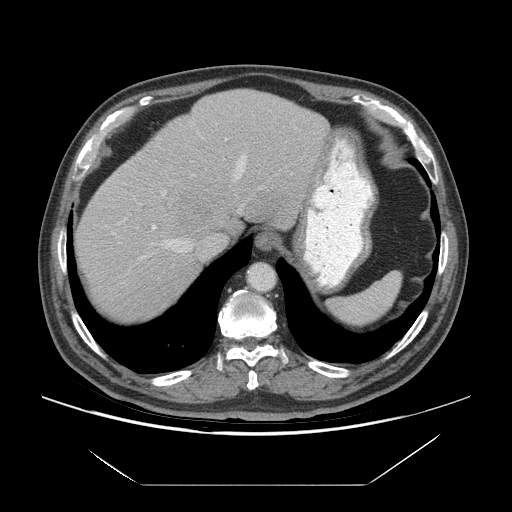
Contrast-enhanced abdominal CT (liver protocol), one axial slice. Slice 55 of 75 in the series (ordered by position). 140 kVp. Soft-tissue window (W 400 / L 40 HU). 512 × 512 image matrix, field of view 420 × 420 mm. From the clinical record (not read from this slice): diagnosis: hepatocellular carcinoma (patient treated with transarterial chemoembolisation; whether this scan precedes or follows treatment is not stated here); TNM stage (as recorded): Stage-I; Child-Pugh class: A; tumour differentiation: well differentiated; tumour size: 5.8 cm.
Structures marked on this image (semi-automatic segmentation, software-assisted and operator-edited):
- abdominal aorta: box from (x=248, y=264) to (x=274, y=291) px
- liver parenchyma outside the tumour (the mass and vessels are separate outlines, so this box may not span the whole liver): (x=76, y=88)–(x=328, y=320)
- mass: (x=173, y=188)–(x=215, y=232)
- liver vessels: (x=114, y=138)–(x=246, y=260)